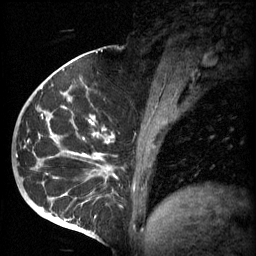
Breast MRI (dynamic contrast-enhanced), one sagittal slice. Position 27 of 60 along the scan axis. 3 images stored at this slice position (order not interpretable as contrast timing). 1.5 T. TE 4.2 ms, TR 11 ms. 2 mm slice thickness. 256 × 256 image matrix, field of view 200 × 200 mm. Patient: female, 51 years.
Structures marked on this image (semi-automatically segmented with operator editing):
- analysis volume of interest (the breast-tissue region the enhancement analysis was run in; not a lesion): box from (x=48, y=82) to (x=161, y=197) px
- tumour enhancement mask (voxels above the 70 % enhancement threshold inside the analysis volume of interest): (x=48, y=92)–(x=160, y=197)